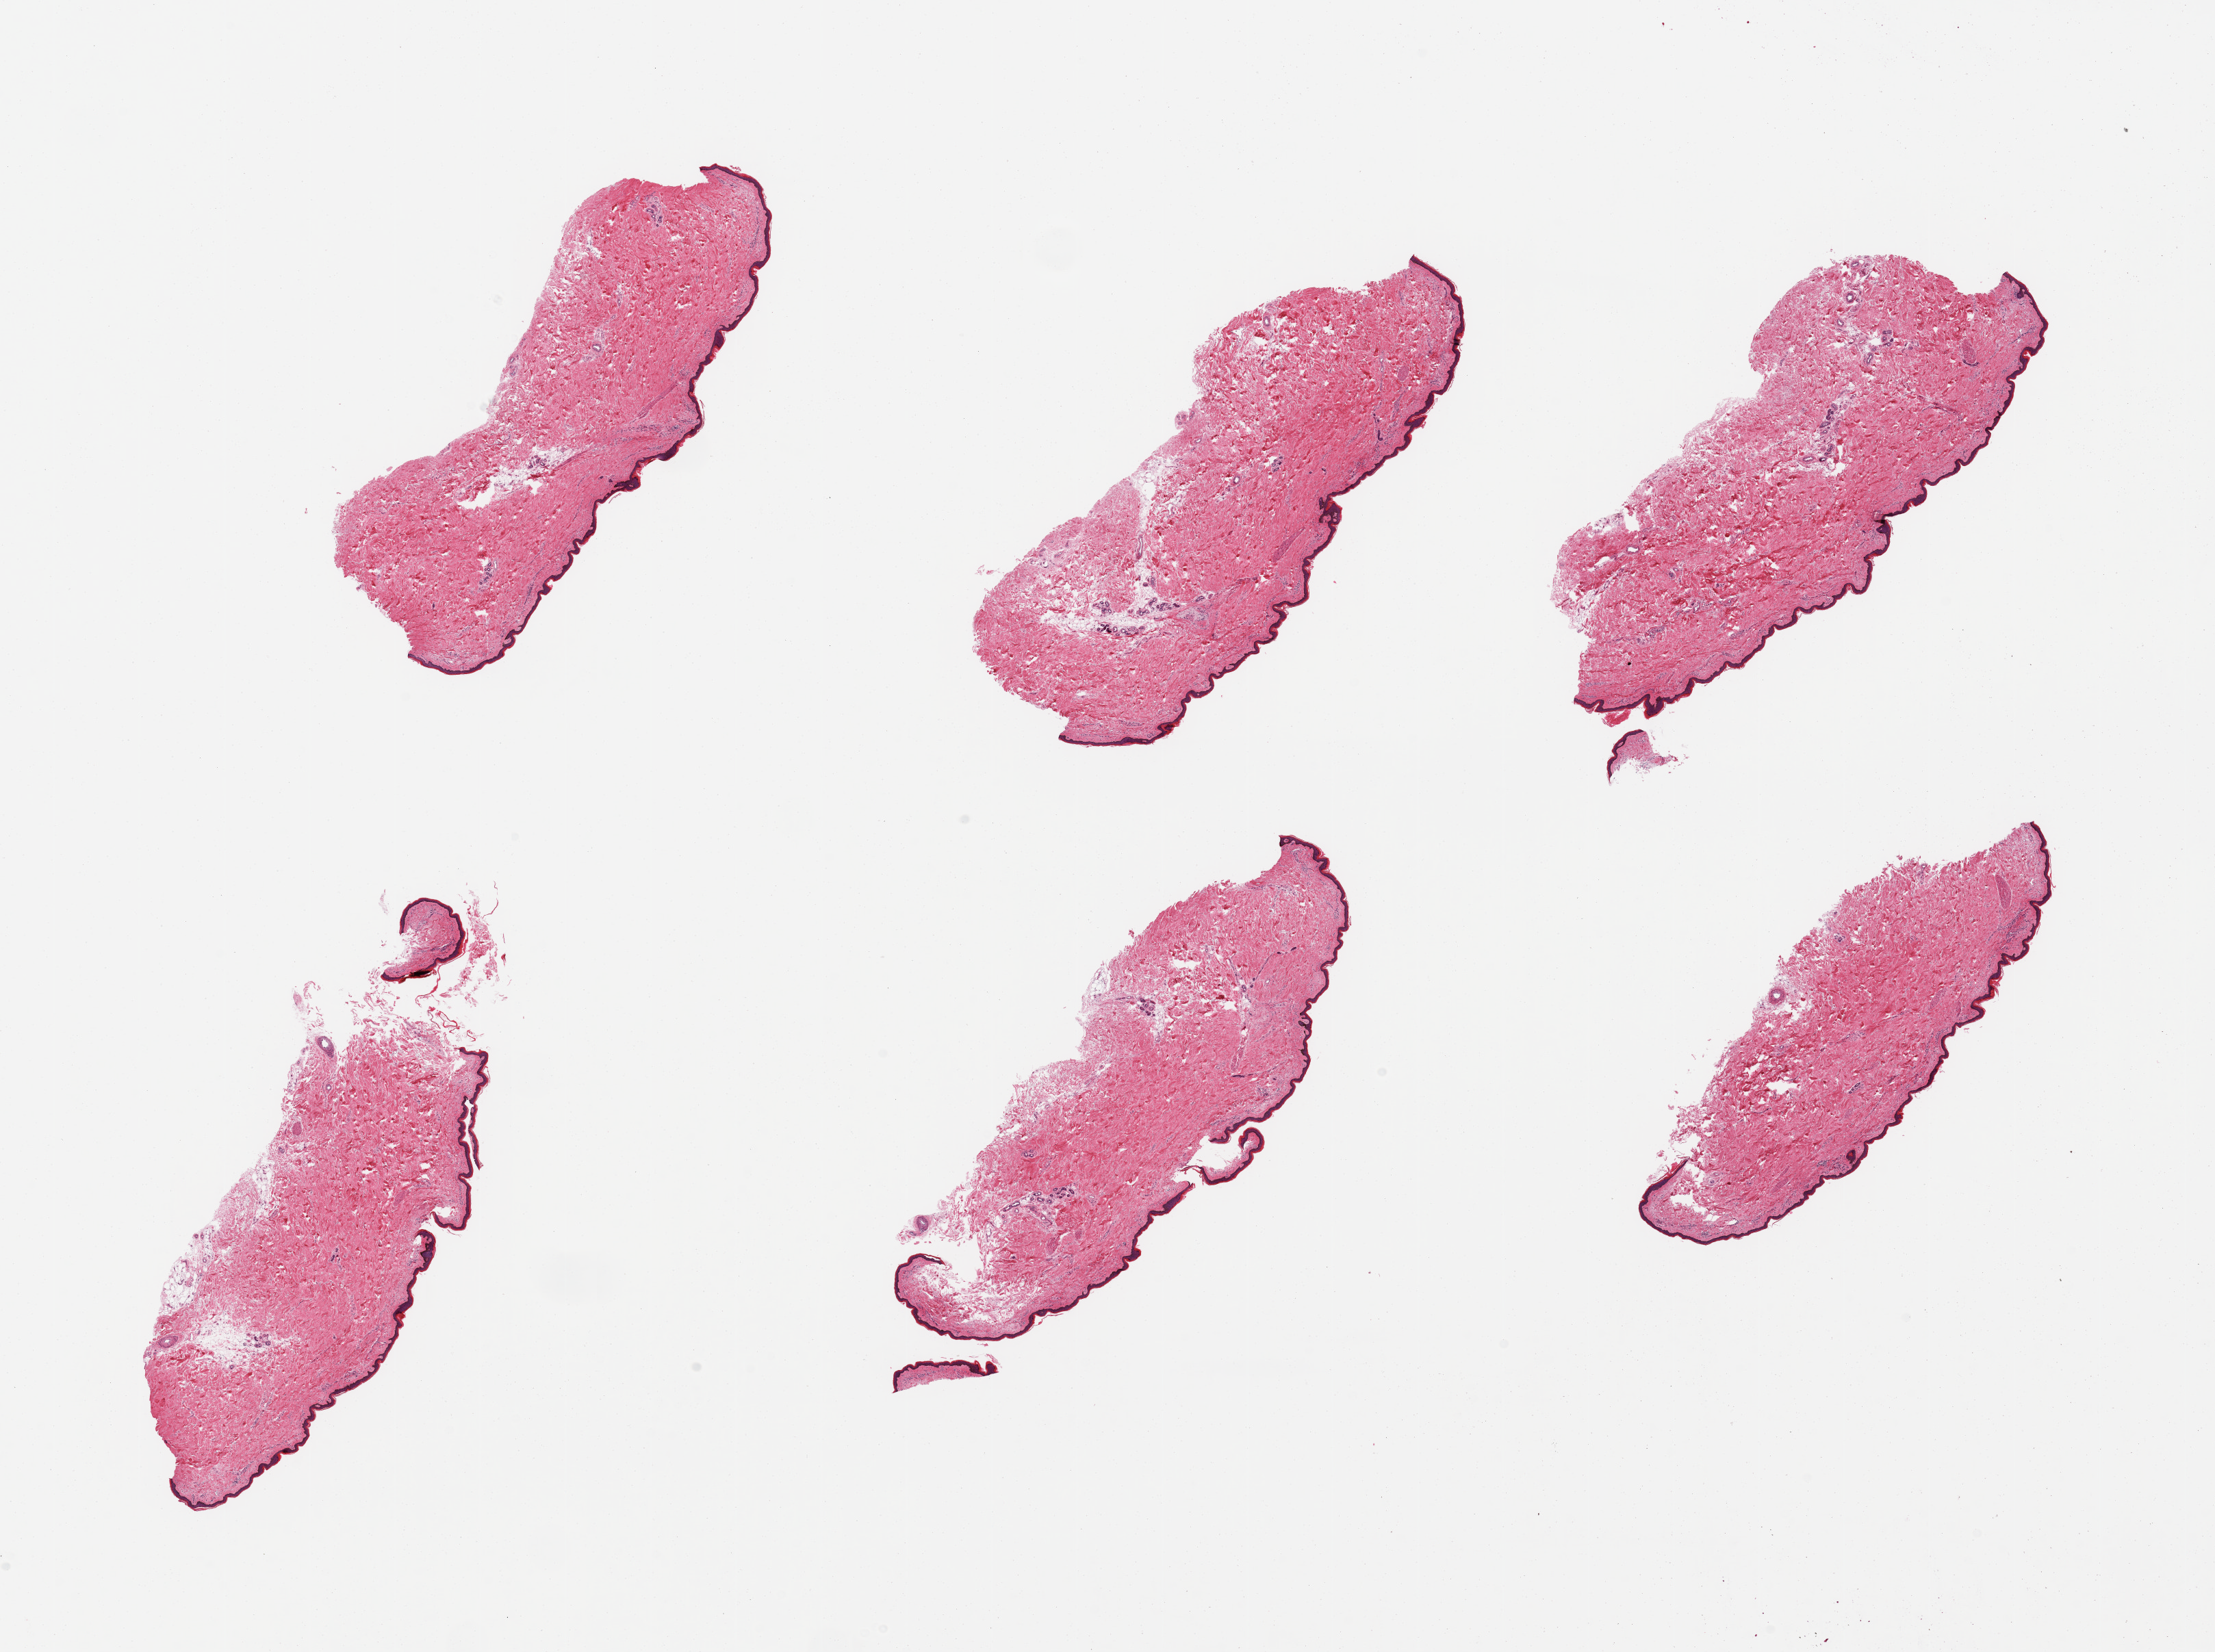
H&E whole-slide image — shown as a low-resolution overview of the whole scanned area (about 25.6 x 19.1 mm); PAXgene-fixed, paraffin-embedded tissue; section of skin of lower leg (target tissue); tissue donor sample. Male donor.
• reviewer comment on this tissue sample: 6 pieces; ~5% internal (periadnexal) fat; epidermis ~ 34um